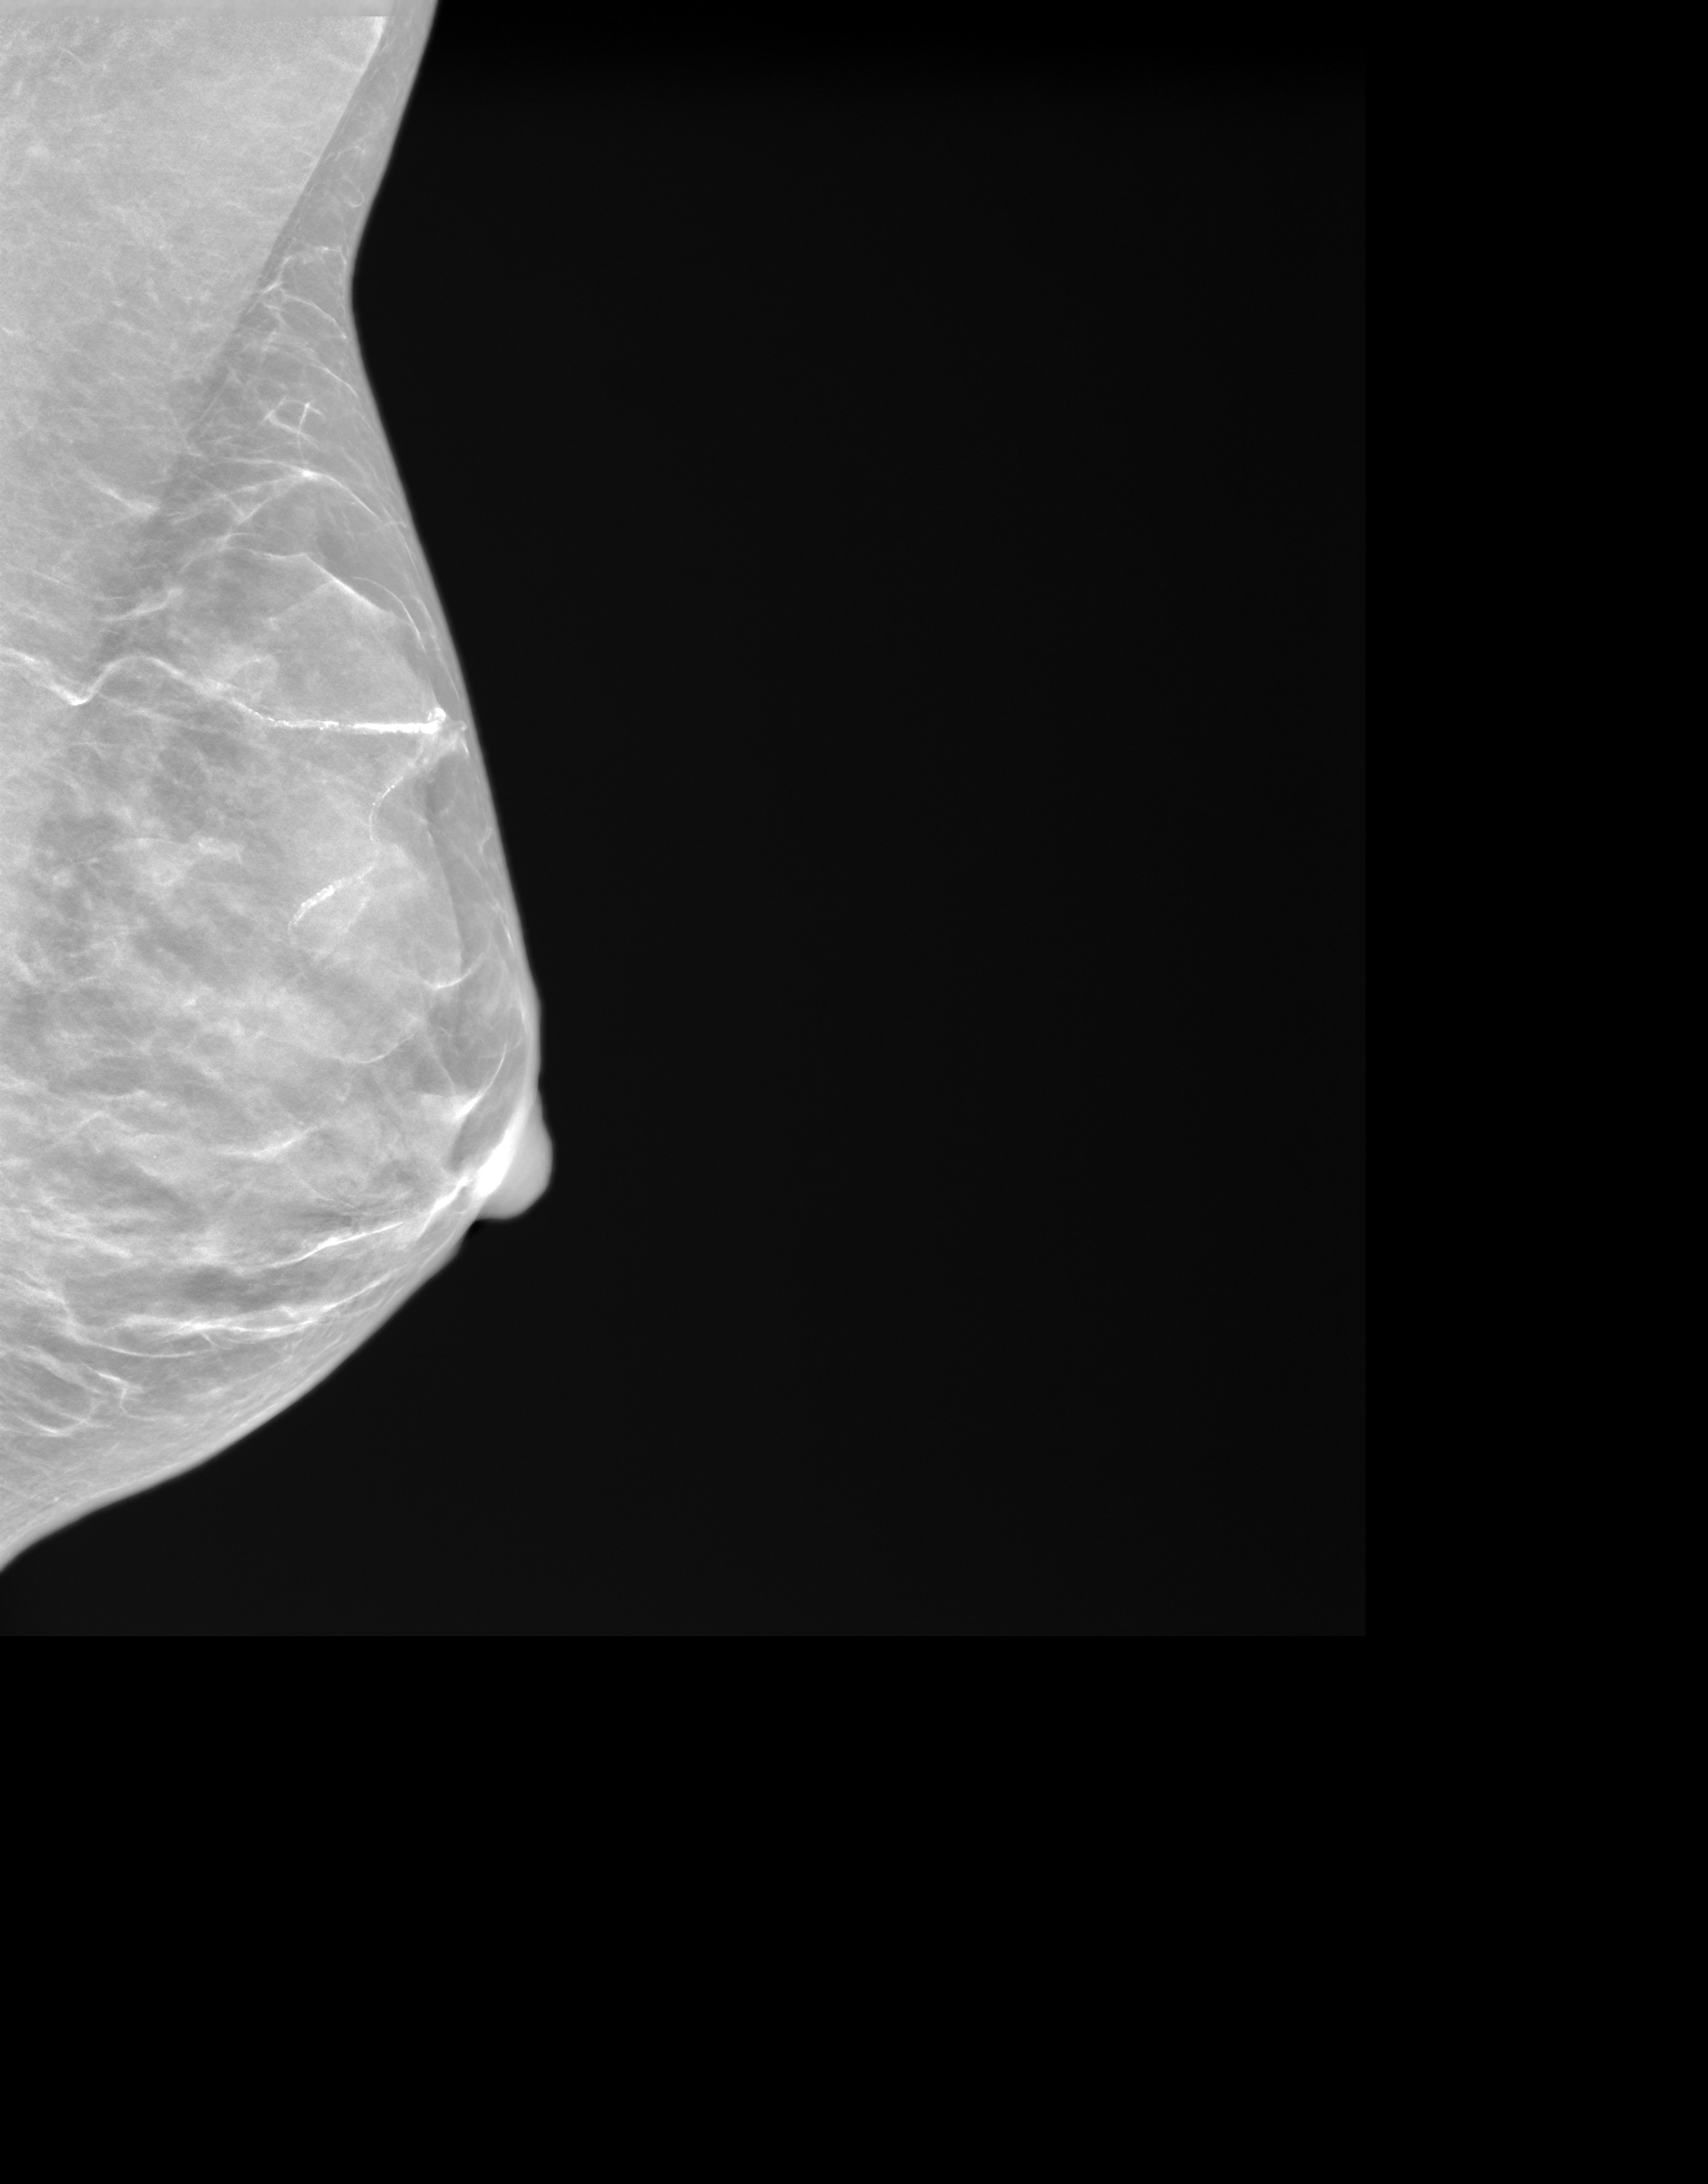
Annual screening mammography examination; system: SenoIris_1SP2(440). Patient: female, 60 years.
Image type: synthesized 2-D view from tomosynthesis. Breast: left. Projection: MLO view.